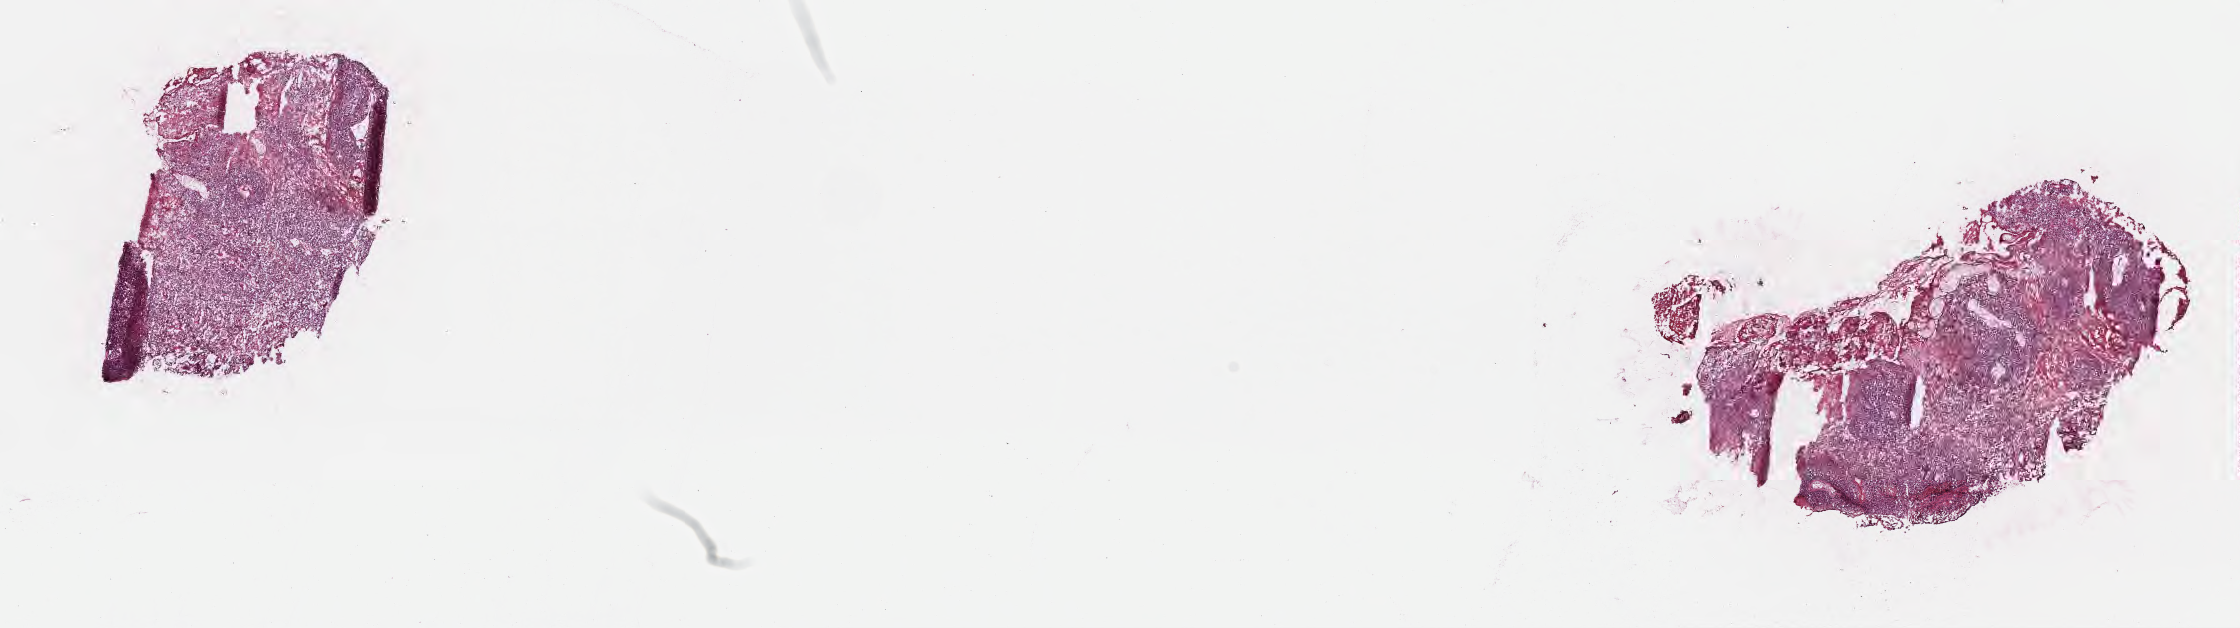
Digitized haematoxylin and eosin-stained section — whole scanned area (about 18.1 x 5.1 mm) shown as a low-resolution overview. Cryosection. Metastatic tumor tissue, resected from brain. Female, age 60 years at initial diagnosis.
Patient diagnosis (primary): Malignant melanoma, NOS.